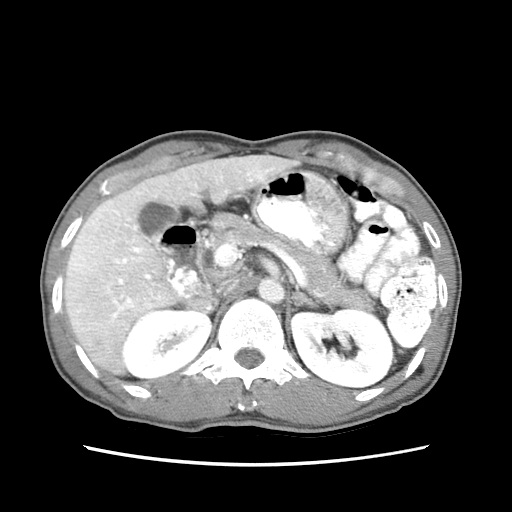
Contrast-enhanced abdominal CT (liver protocol), one axial slice; position 36 of 79 along the scan axis; reconstruction kernel STANDARD; 120 kVp; soft-tissue window (W 400 / L 40 HU); 2.5 mm slice thickness; 512 × 512 image matrix, field of view 320 × 320 mm. Case-level facts recorded for this patient, not image findings: diagnosis: hepatocellular carcinoma (patient treated with transarterial chemoembolisation; whether this scan precedes or follows treatment is not stated here); TNM stage (as recorded): Stage-IIIB; Child-Pugh class: A; tumour differentiation: moderately differentiated; tumour nodularity: multinodular.
Structures marked on this image (semi-automatic segmentation, software-assisted and operator-edited):
- liver parenchyma outside the tumour (the mass and vessels are separate outlines, so this box may not span the whole liver): bounding box <64,152,300,376> (left, top, right, bottom; pixels)
- mass: <69,254,98,269>
- liver vessels: <73,164,284,331>